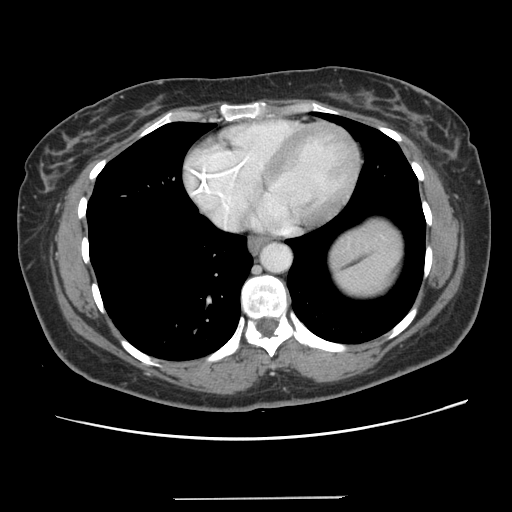
Contrast-enhanced abdominal CT, one axial slice; position 129 of 141 along the scan axis; intravenous contrast given; soft-tissue window (W 400 / L 40 HU); 2.5 mm slice thickness; 512 × 512 image matrix, field of view 366 × 366 mm. Female patient, age 53 years. From the clinical record (not read from this slice): diagnosis: colorectal cancer liver metastases, imaged before liver resection; multiple liver metastases: no; largest metastasis: 14.5 cm; disease in both lobes: yes.
Structures marked on this image (expert manual segmentation):
- liver: bounding box [x1, y1, x2, y2] px = [356, 223, 384, 238]